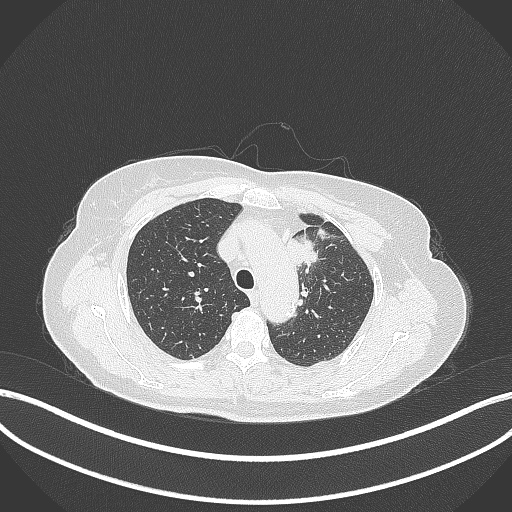
Chest CT, one axial slice; slice 254 of 369 in the series (ordered by position); reconstruction kernel B70f; 120 kVp; lung window (W 1500 / L -600 HU); 1 mm slice thickness; 512 × 512 image matrix, field of view 400 × 400 mm. Female patient, age 65 years. From the clinical record (not read from this slice): clinical TNM (as recorded): T2a N0 M0; histopathological grade: G2-3.
Annotated regions visible in this slice (bounding box drawn by a radiologist):
- lung tumour (recorded histology: adenocarcinoma): bounding box [x1, y1, x2, y2] px = [285, 231, 320, 271]